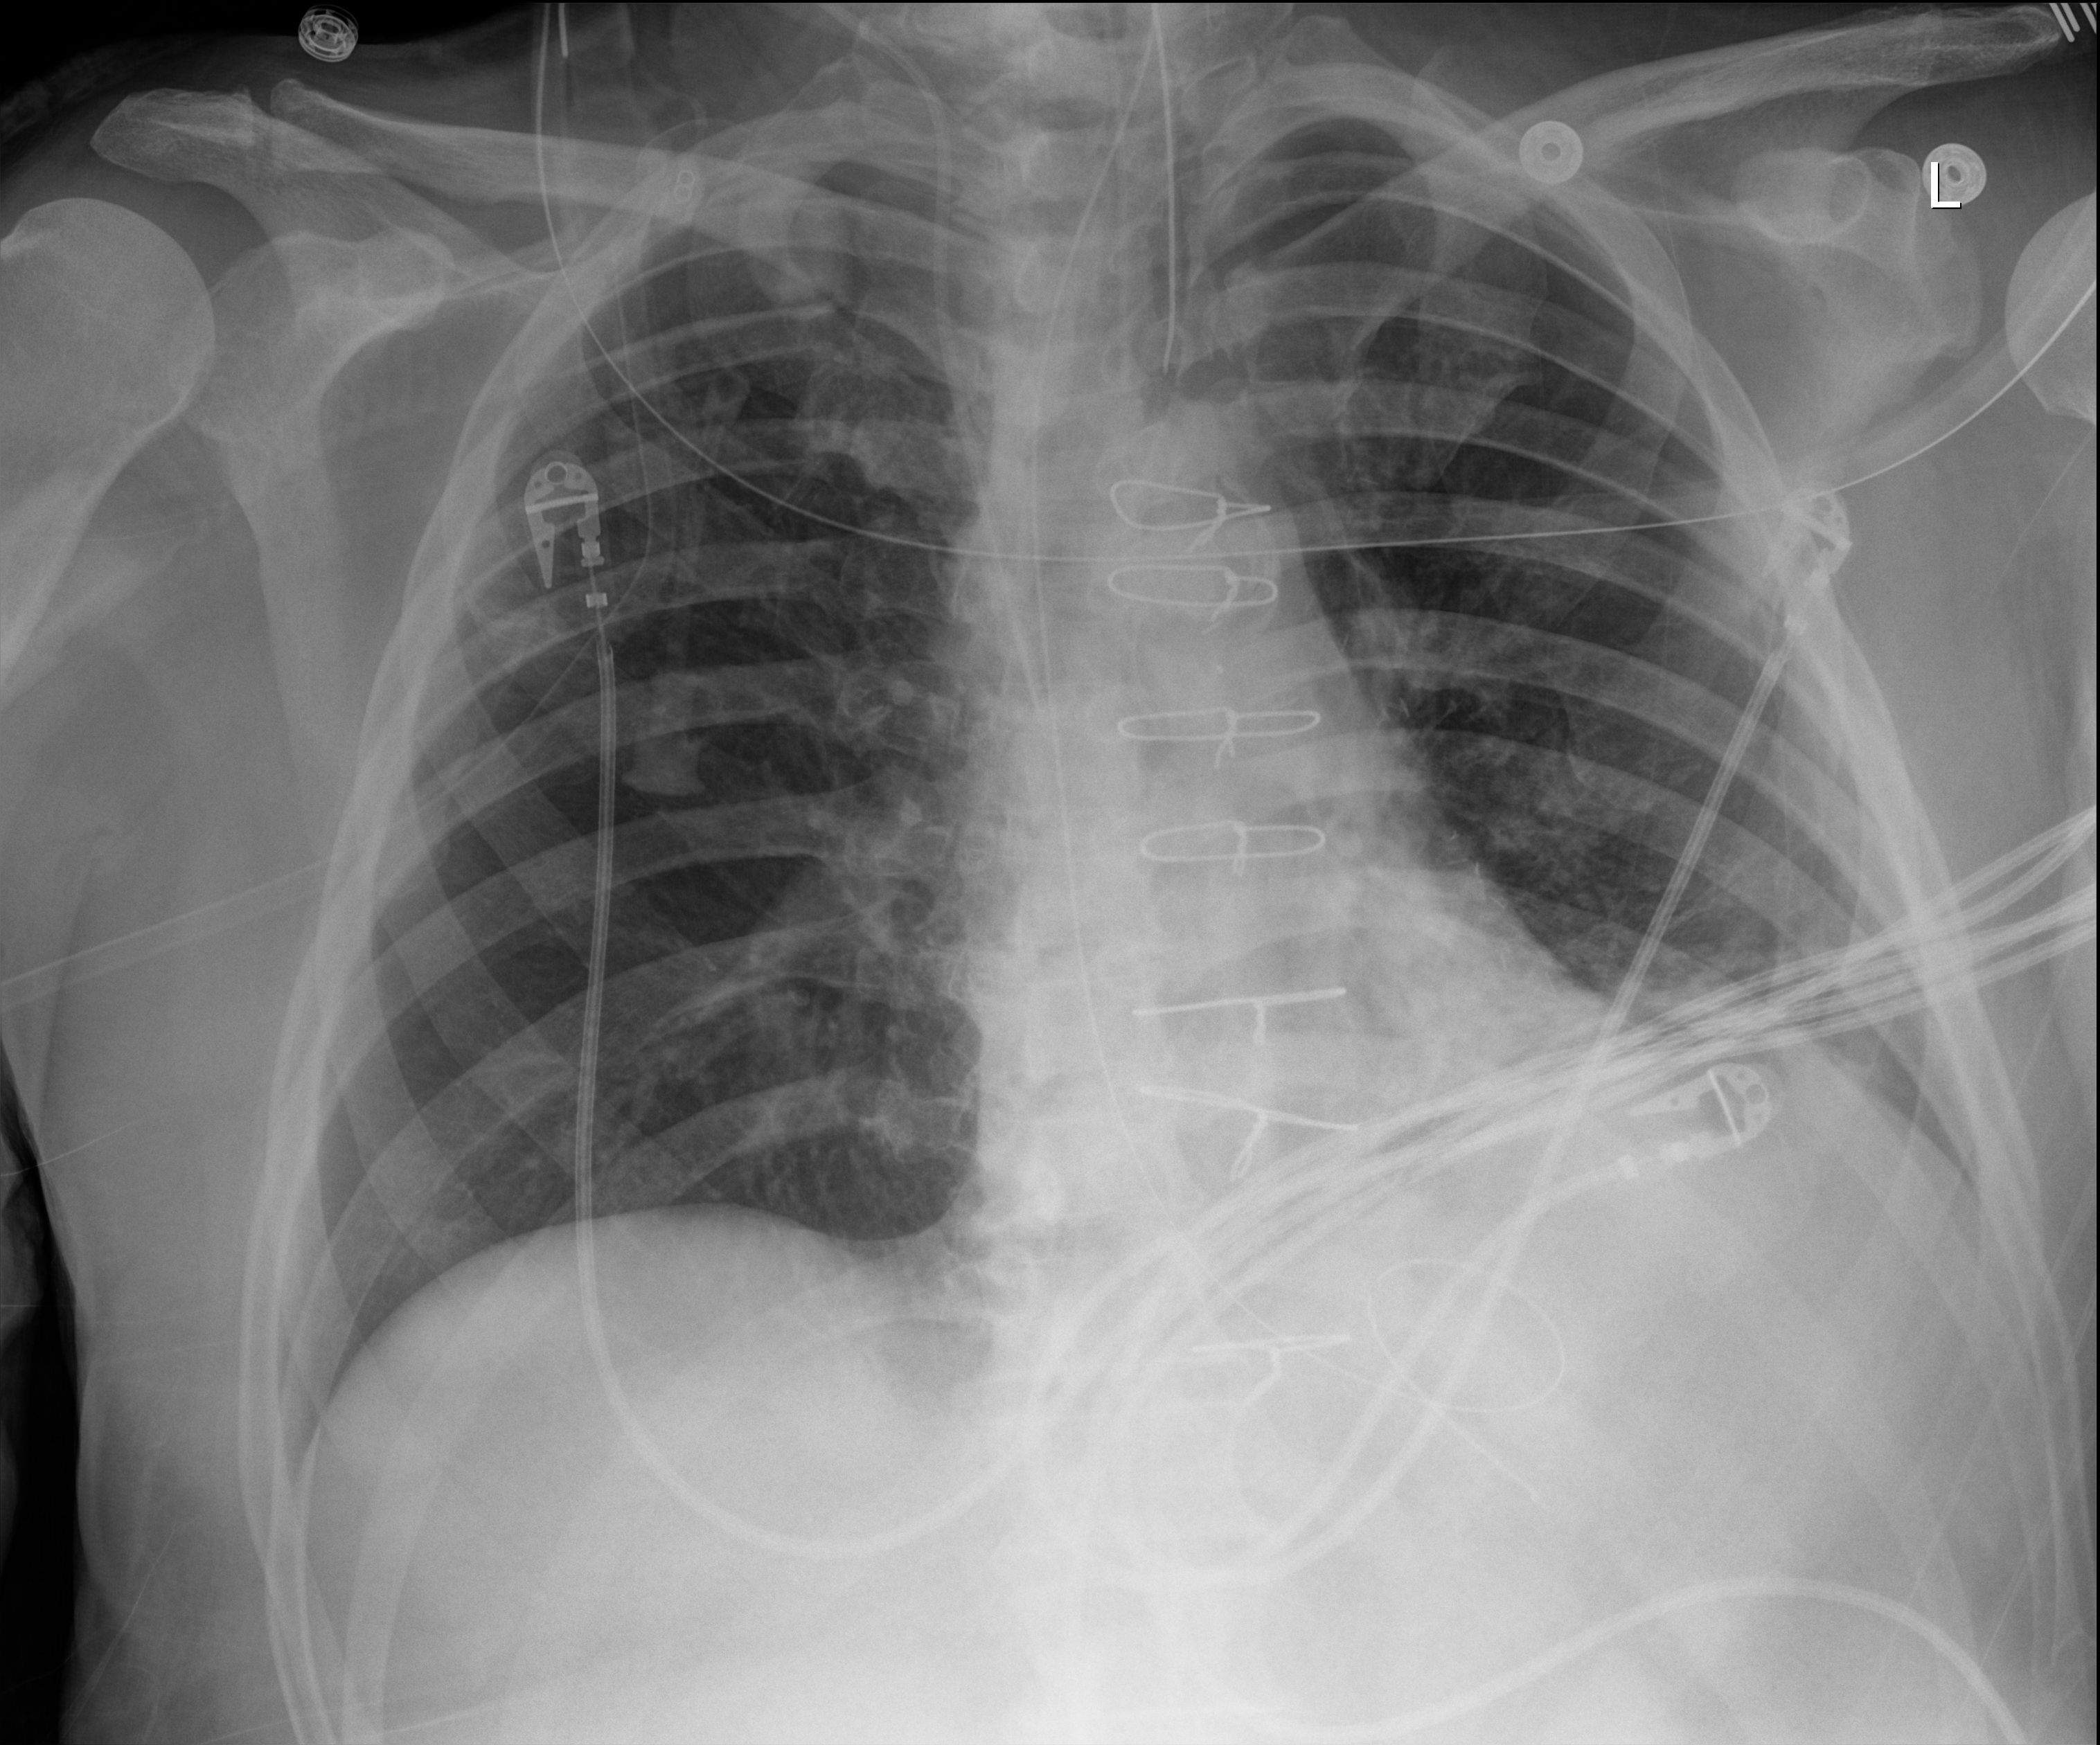
Chest X-ray (portable), anteroposterior (AP) projection. Male patient hospitalised with COVID-19, age 60–74 years.
Hospital-stay facts (about this admission, not read from this image; timing relative to this image not recorded):
- diabetes (admission record): yes
- mechanically ventilated during this hospital stay: yes
- admitted to intensive care during this hospital stay: yes